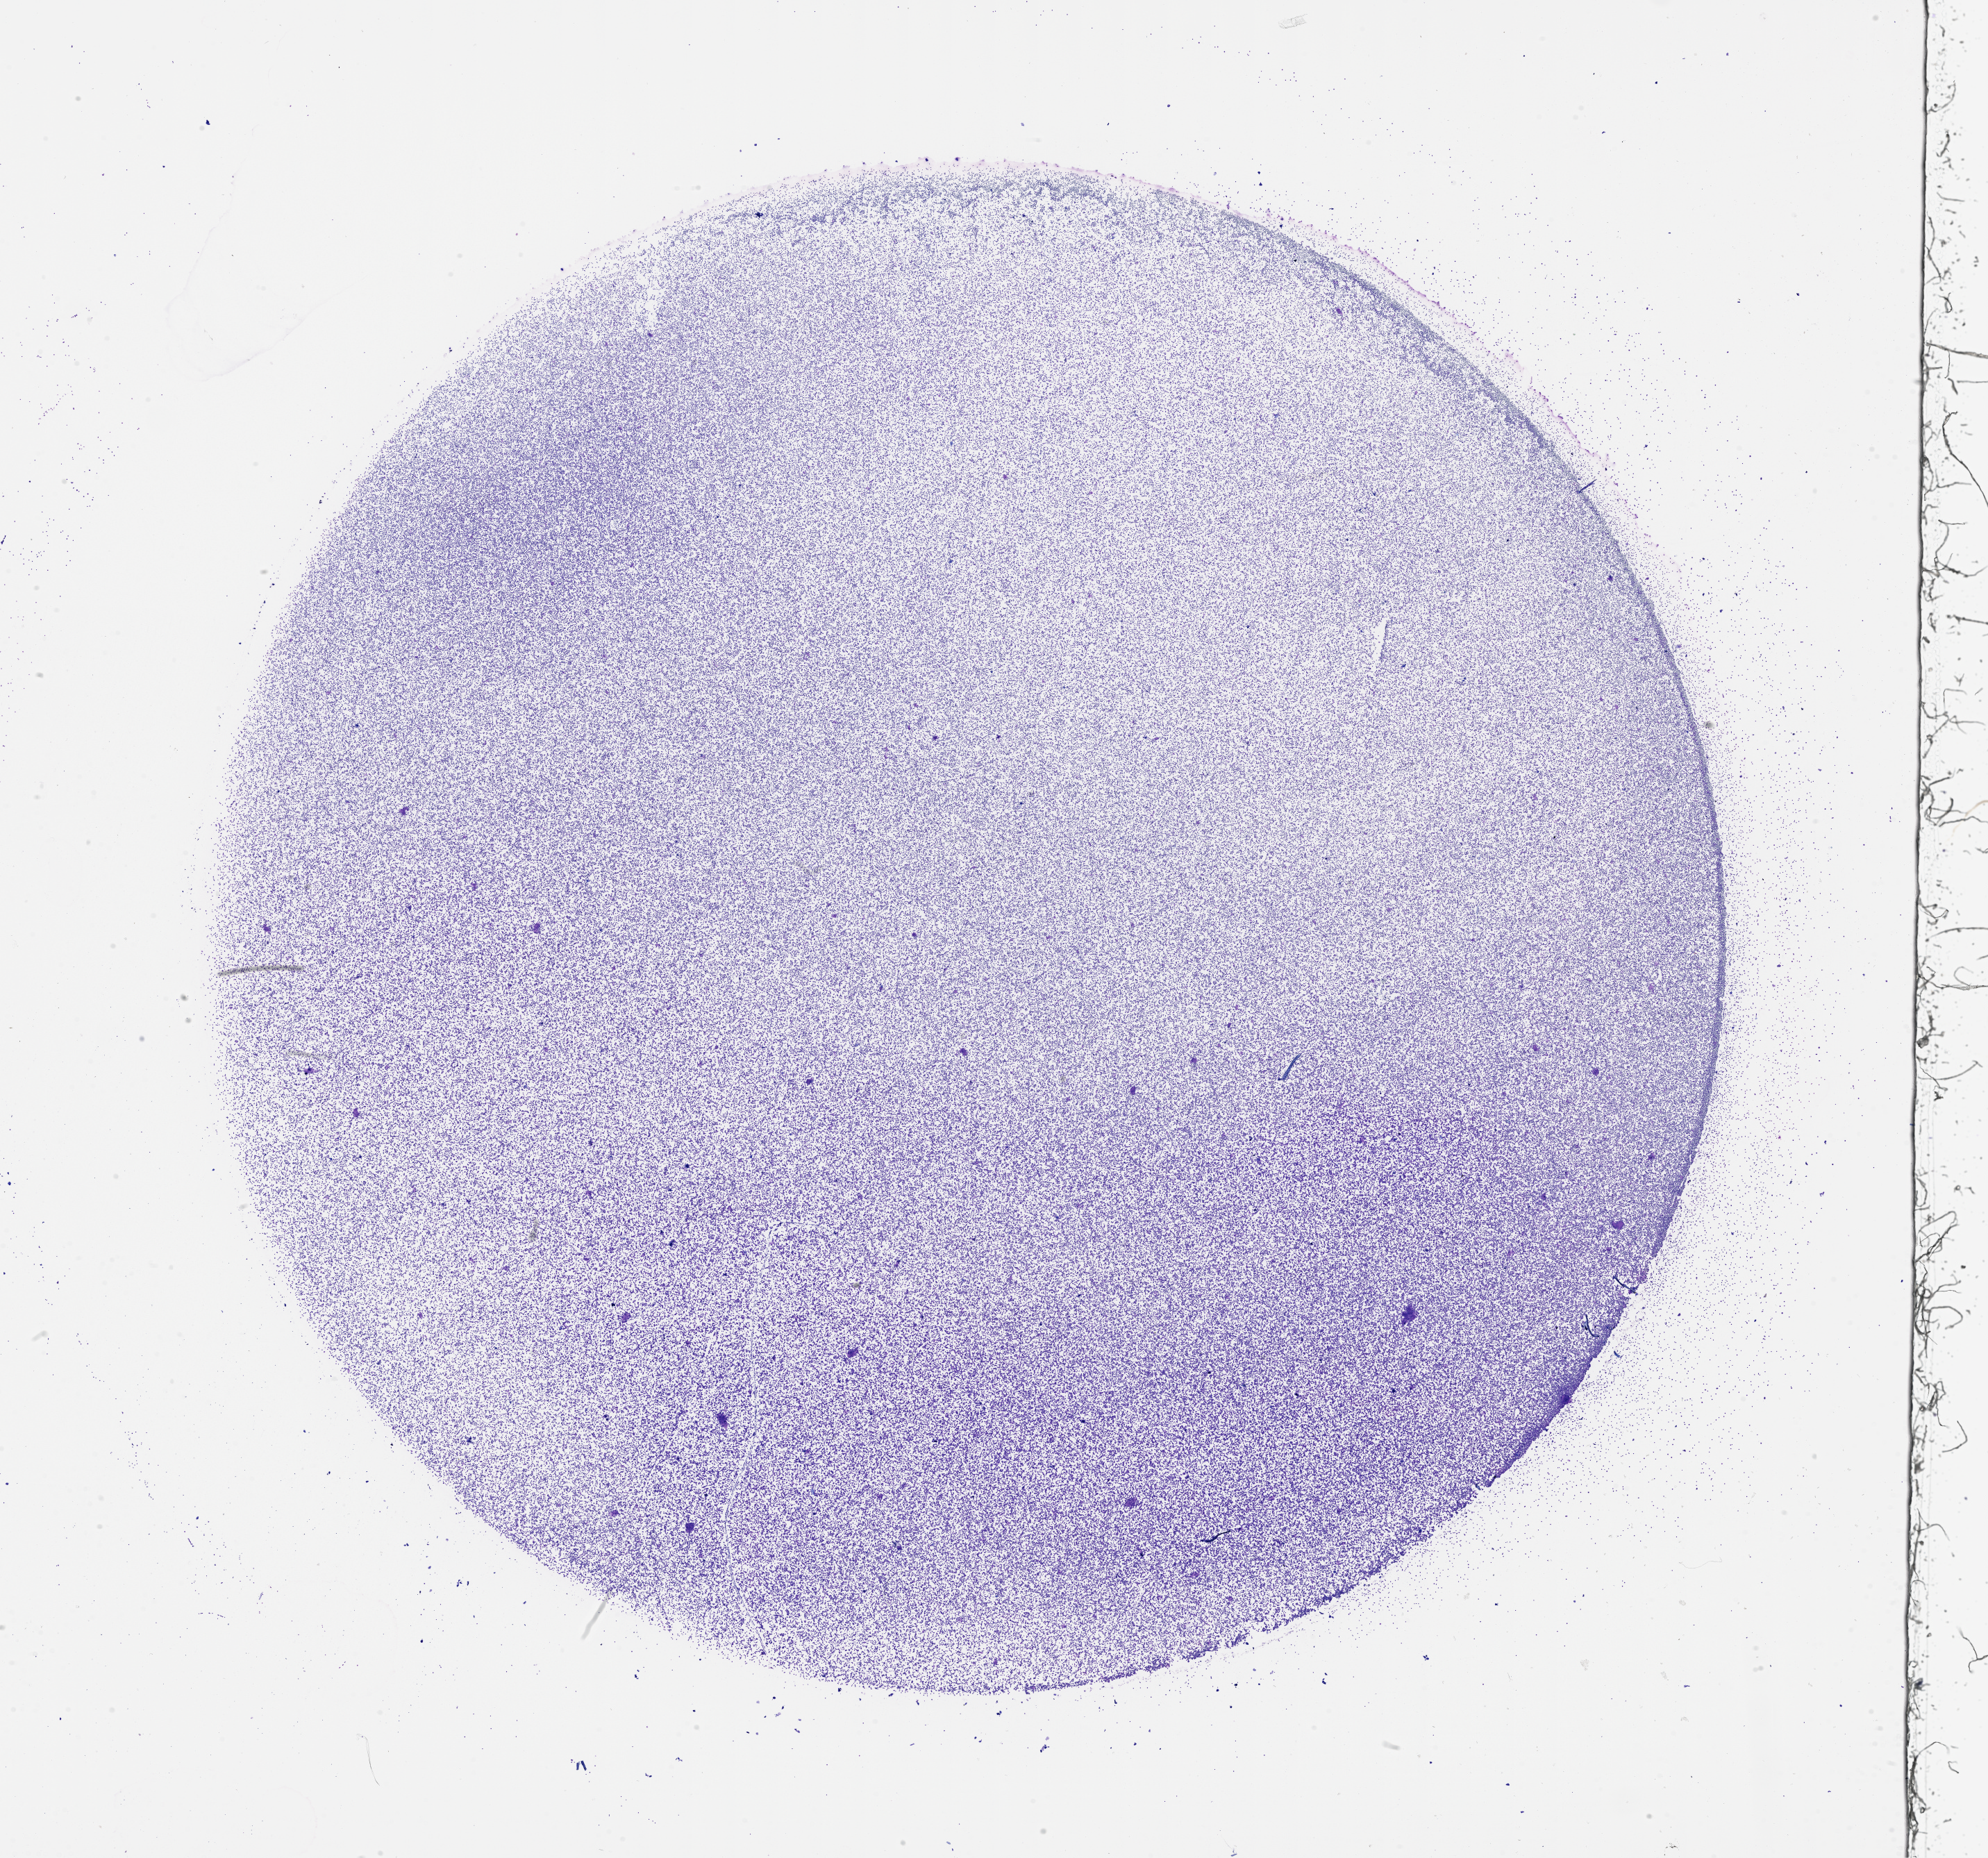
Whole-slide histology image, Hematoxylin and eosin (H&E) stained — shown as a low-resolution overview of the whole scanned area (about 23.1 x 21.6 mm). Bone marrow (leukaemic) sample. Patient: female, age 60 years. Blasts: 60%.
* FAB classification: M1
* WHO classification: AML without maturation
* diagnosis: Acute Myeloid Leukemia